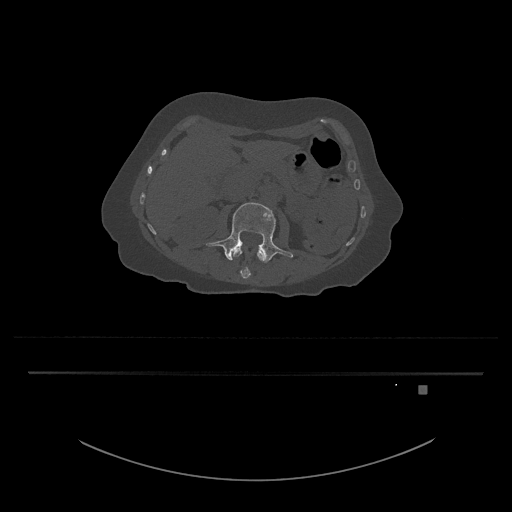
CT including the spine, one axial slice; slice 445 of 797 in the series (ordered by position); reconstruction kernel Br40s/3; 120 kVp; bone window (W 1800 / L 400 HU); 512 × 512 image matrix. Patient: female, 57 years. Case-level facts recorded for this patient, not image findings: primary cancer: cervical.
Outlined on this slice (semi-automatic segmentation, software-assisted and operator-edited):
- L3 vertebra: bounding box [x1, y1, x2, y2] px = [206, 202, 293, 263]